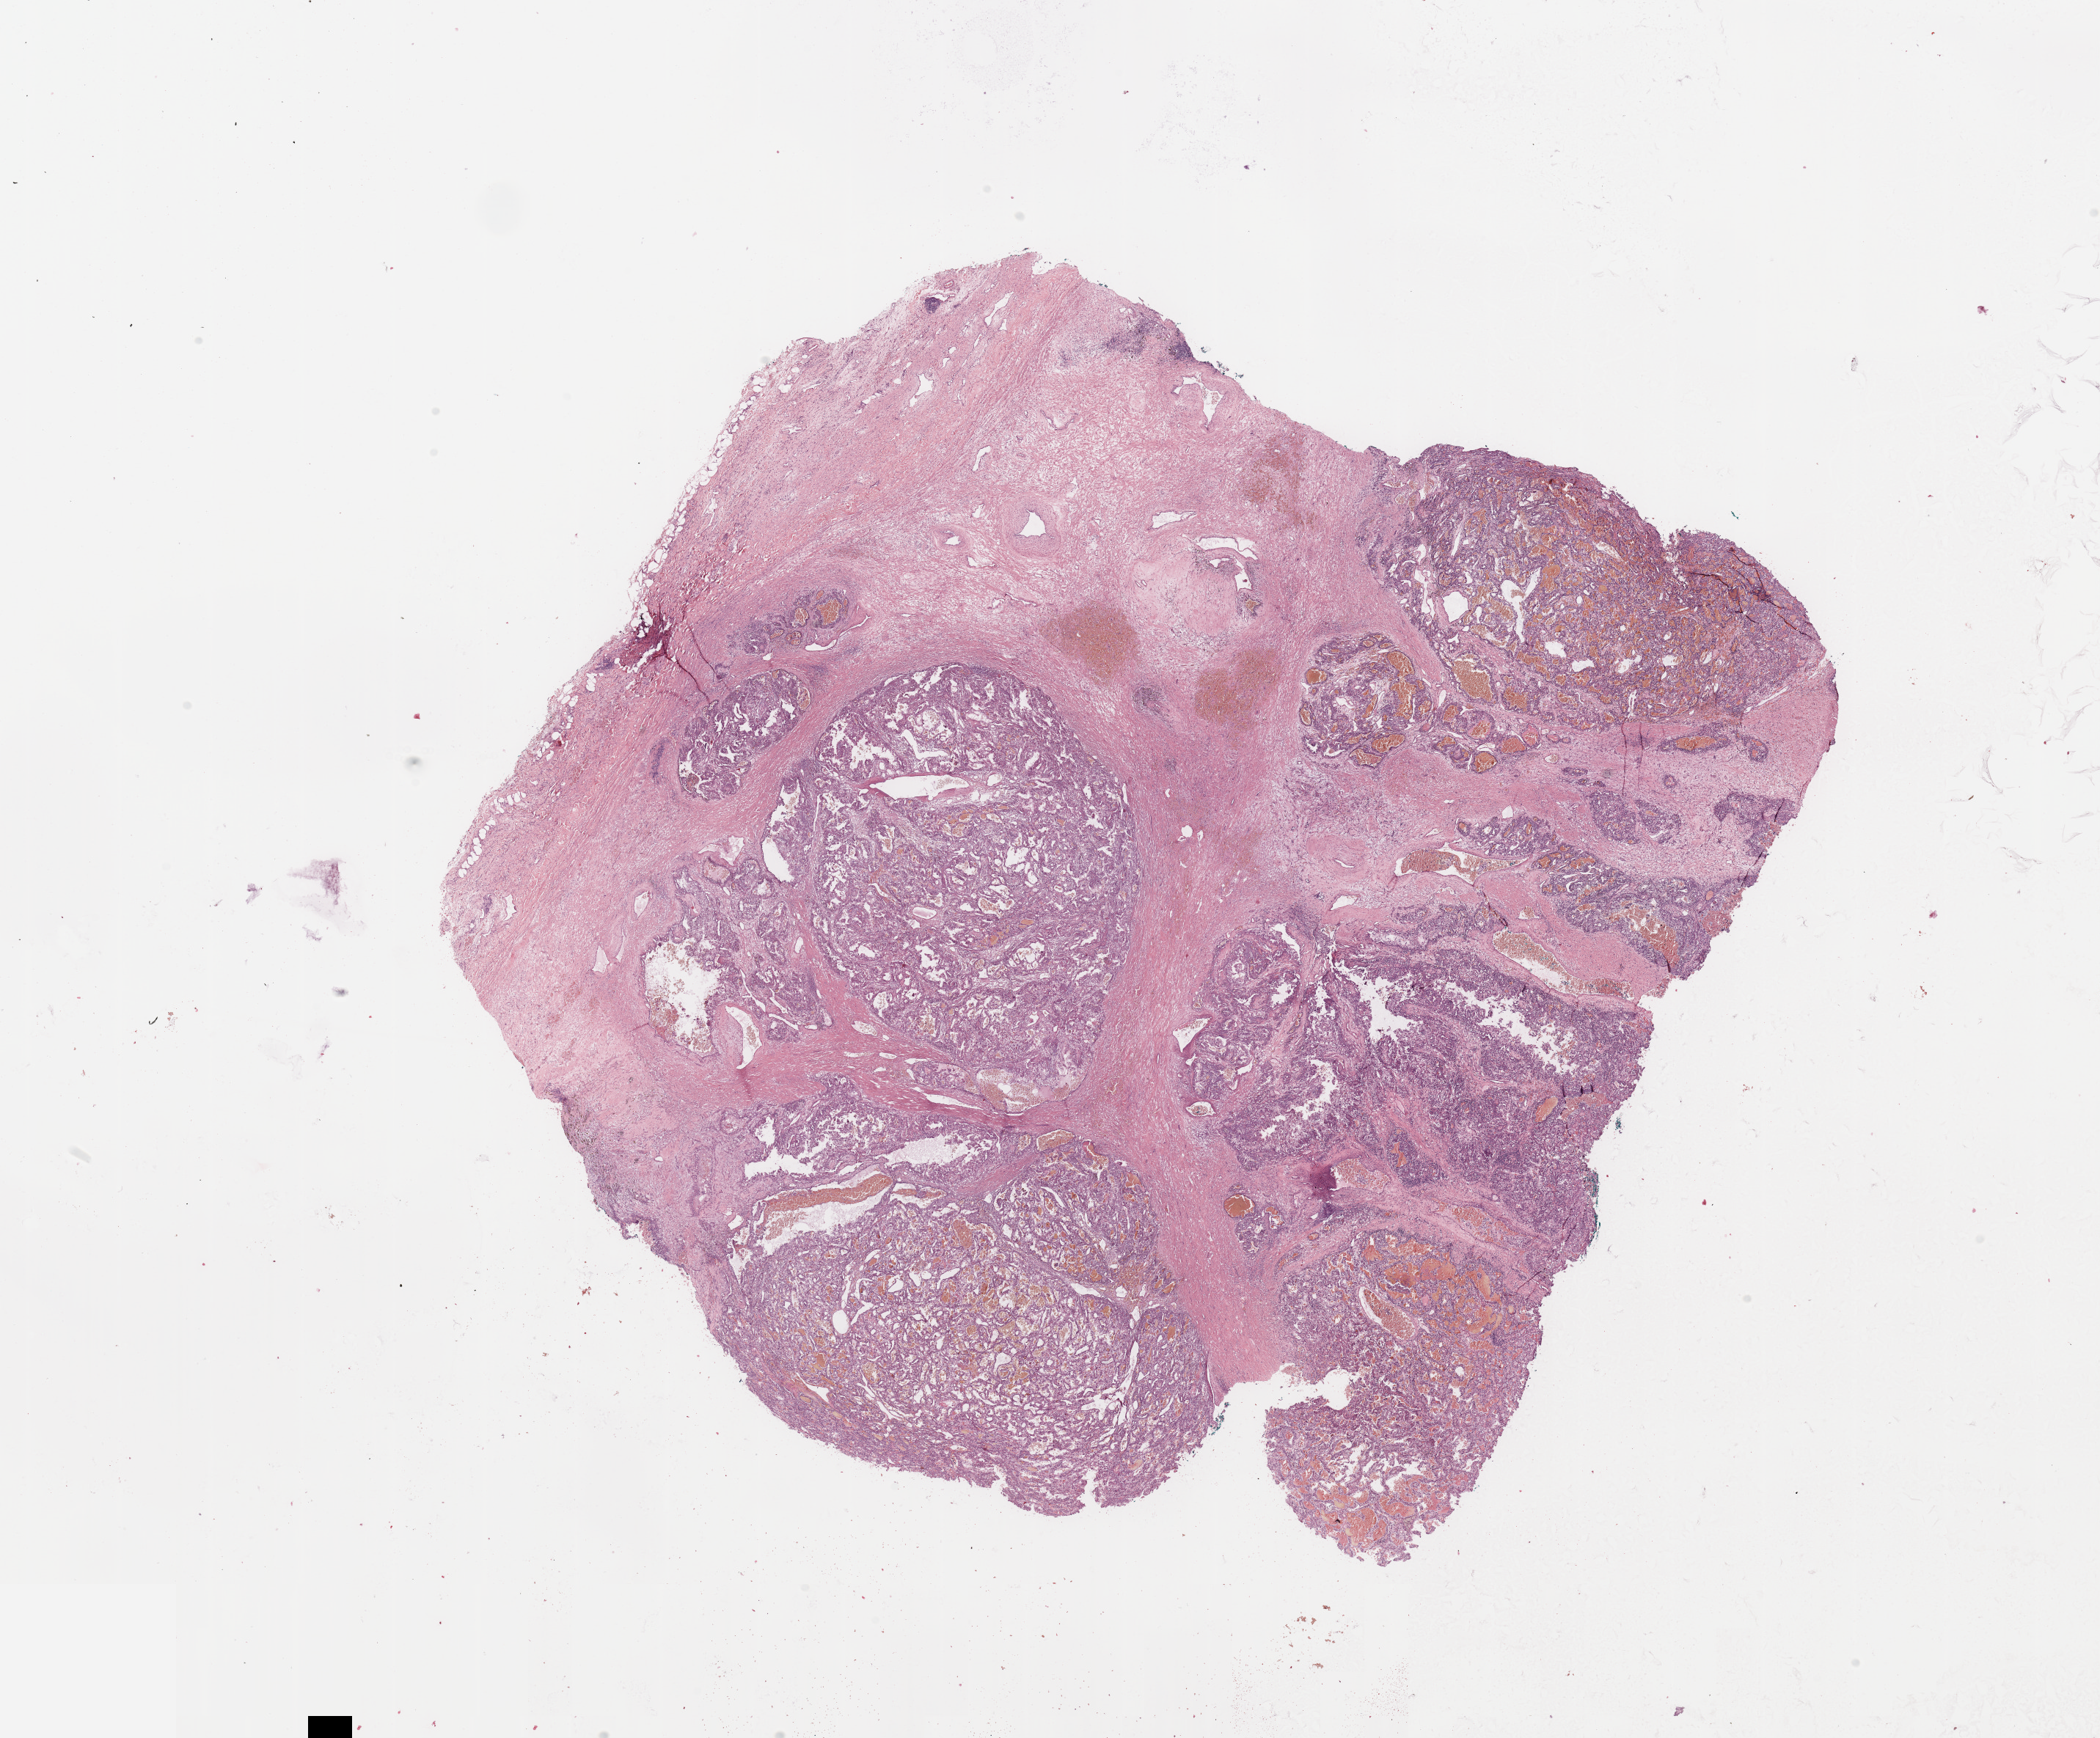
Digitized Hematoxylin and eosin (H&E) stained tissue section (whole slide), shown as a low-resolution overview of the whole scanned area (about 22.6 x 18.7 mm, slide scanned at 20x). Tumour tissue sample, kidney. Male, 45 y/o. Histologic grade: G2 (moderately differentiated).
AJCC pathologic stage: II. Histologic diagnosis: Renal cell carcinoma, NOS. Primary tumour site (as recorded): middle.